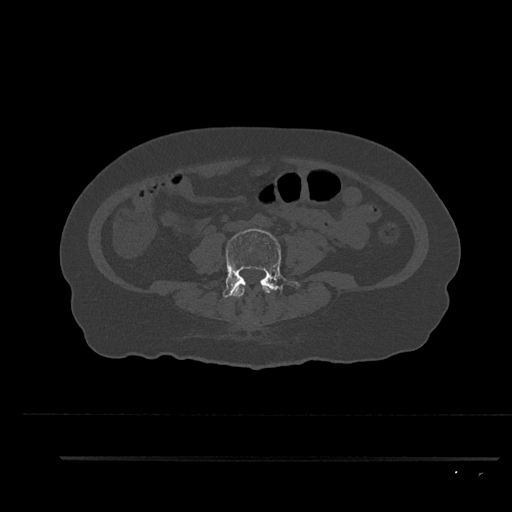
CT including the spine, one axial slice; slice 36 of 797 in the series (ordered by position); reconstruction kernel Br40s/3; bone window (W 1800 / L 400 HU); 512 × 512 image matrix. Female patient, age 44 years. Case-level facts recorded for this patient, not image findings: primary cancer: renal; vertebrae with lytic lesions (as recorded): L1.
Structures marked on this image (semi-automatically segmented with operator editing):
- L3 vertebra: bounding box [x1, y1, x2, y2] px = [232, 284, 271, 298]
- L4 vertebra: [223, 228, 300, 298]